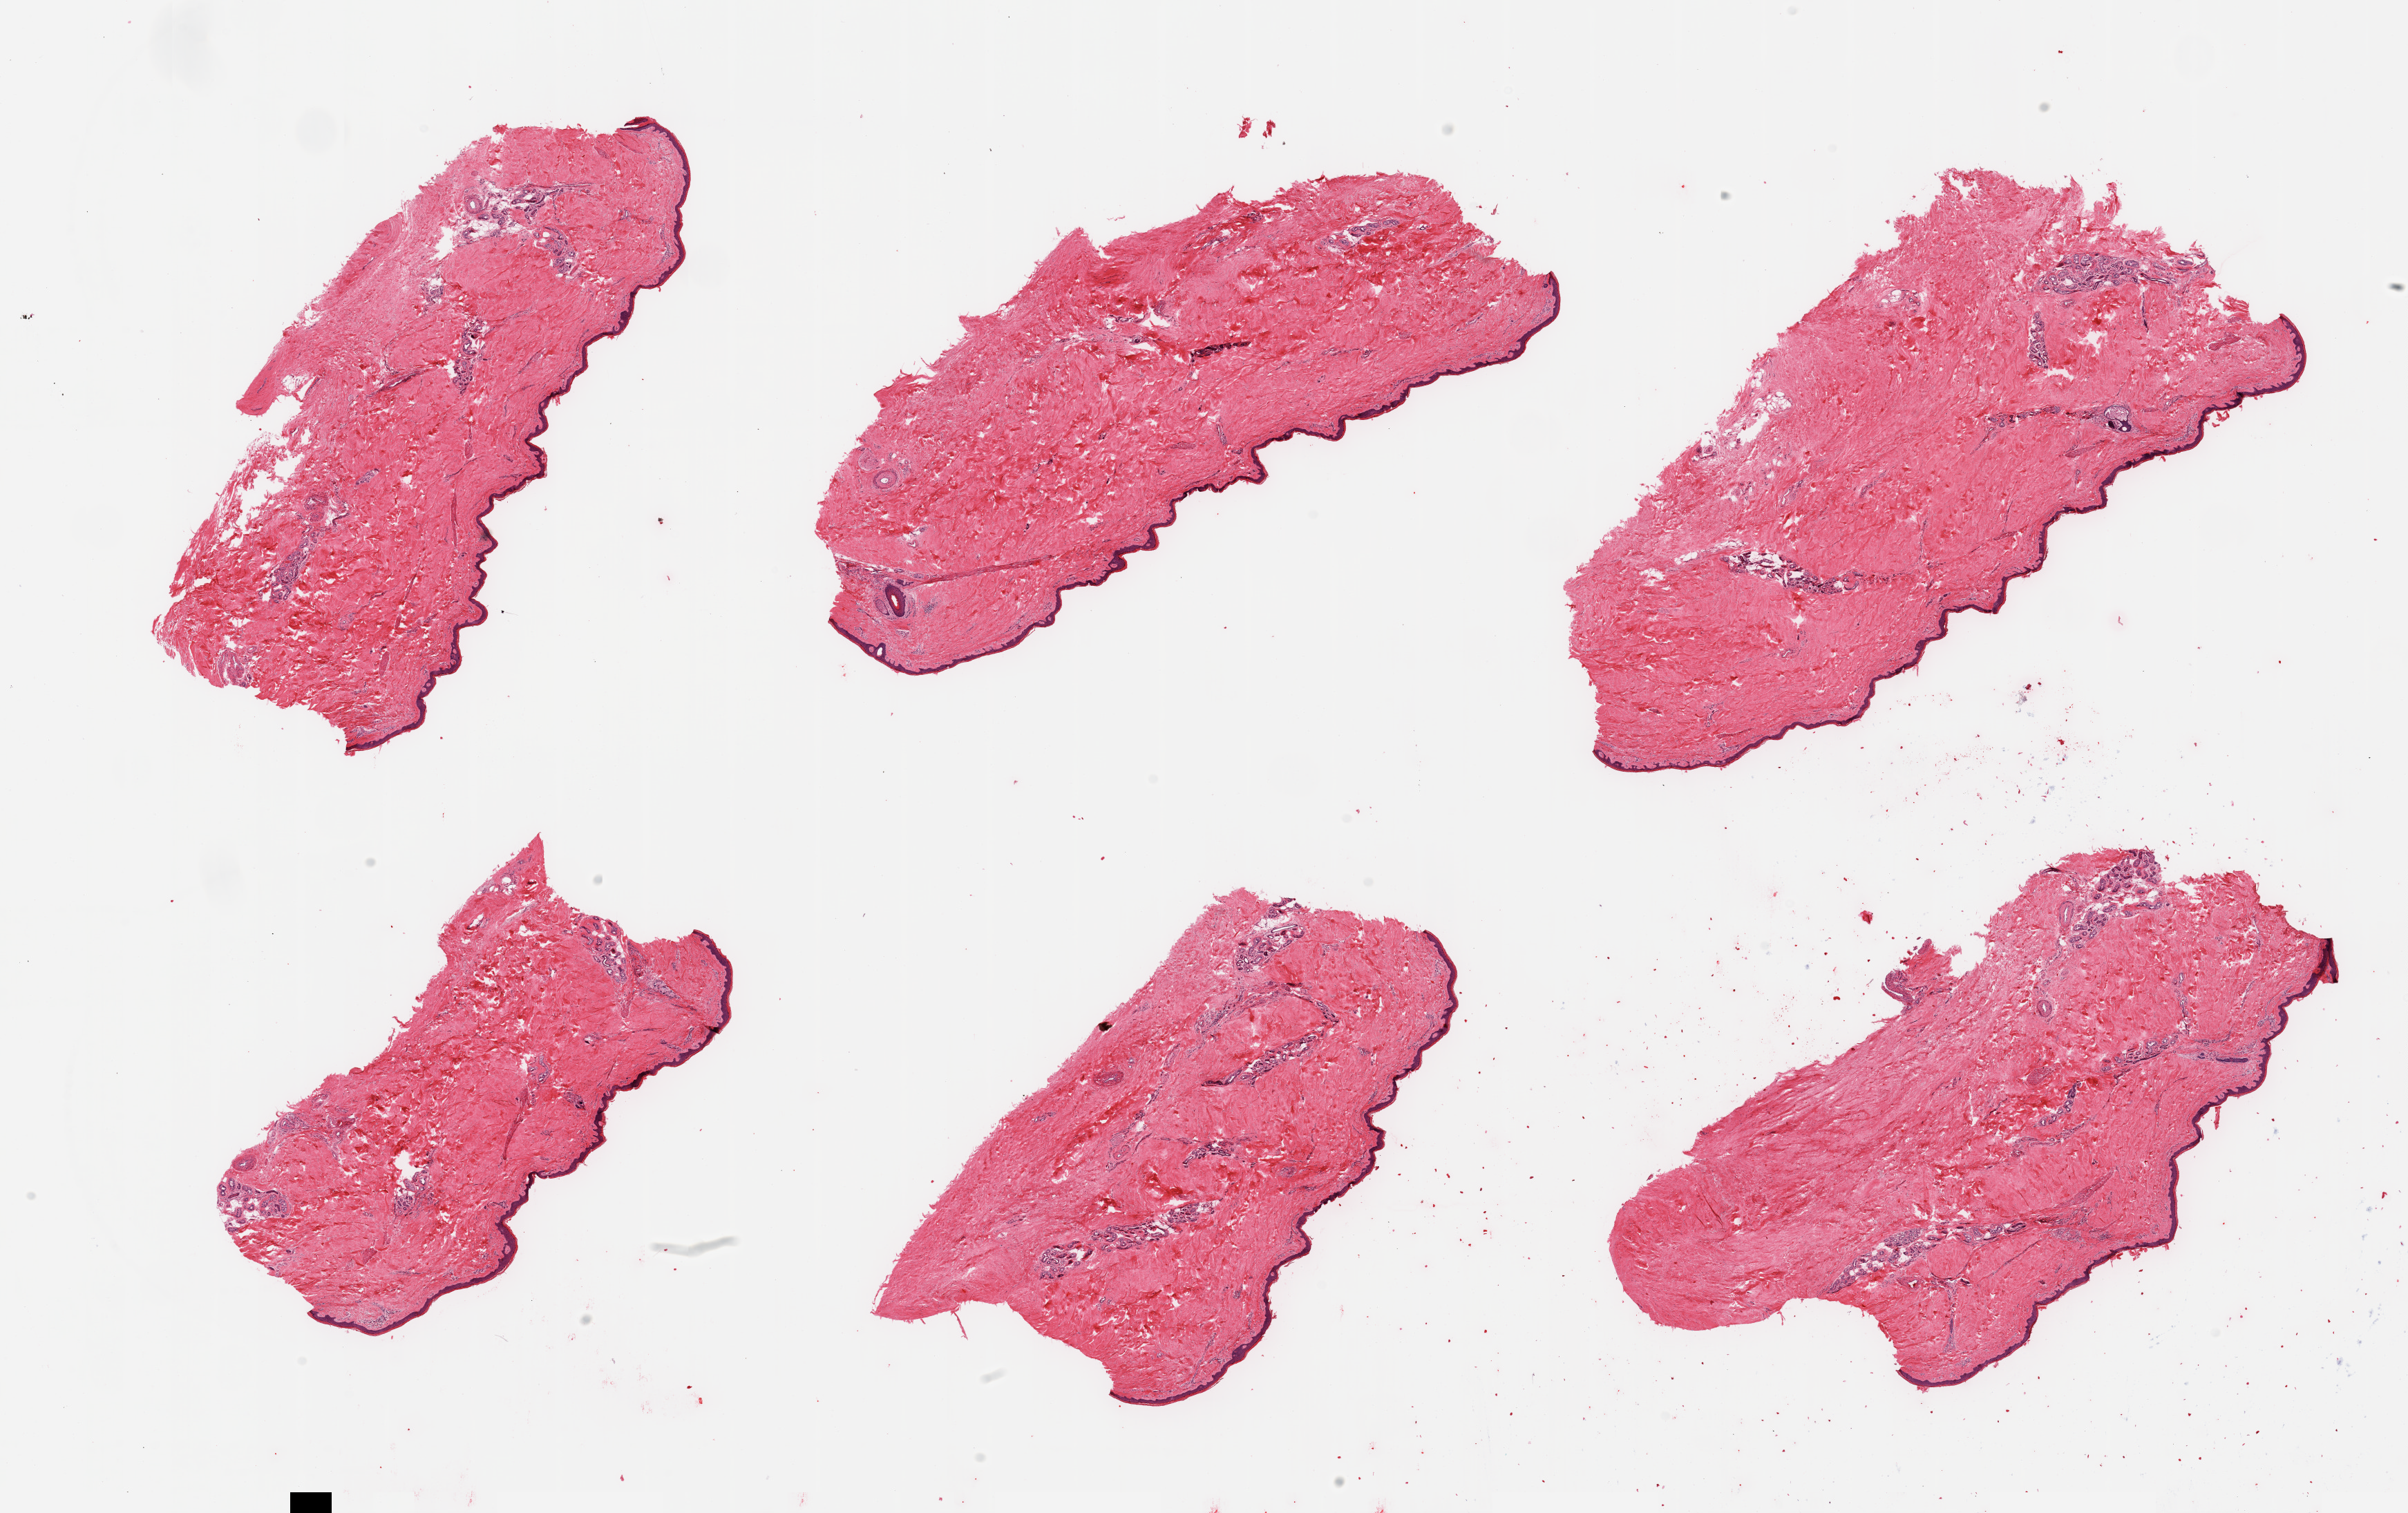
Whole-slide image, hematoxylin and eosin (H&E) stain — whole scanned area (about 27.6 x 17.3 mm) shown as a low-resolution overview, PAXgene-fixed paraffin-embedded (PFPE) section, sampled site (target tissue): skin of lower leg, tissue donor sample. Male donor.
Pathologist's review note for this sample: 6 pieces; well trimmed, epidermis measures 38 microns.